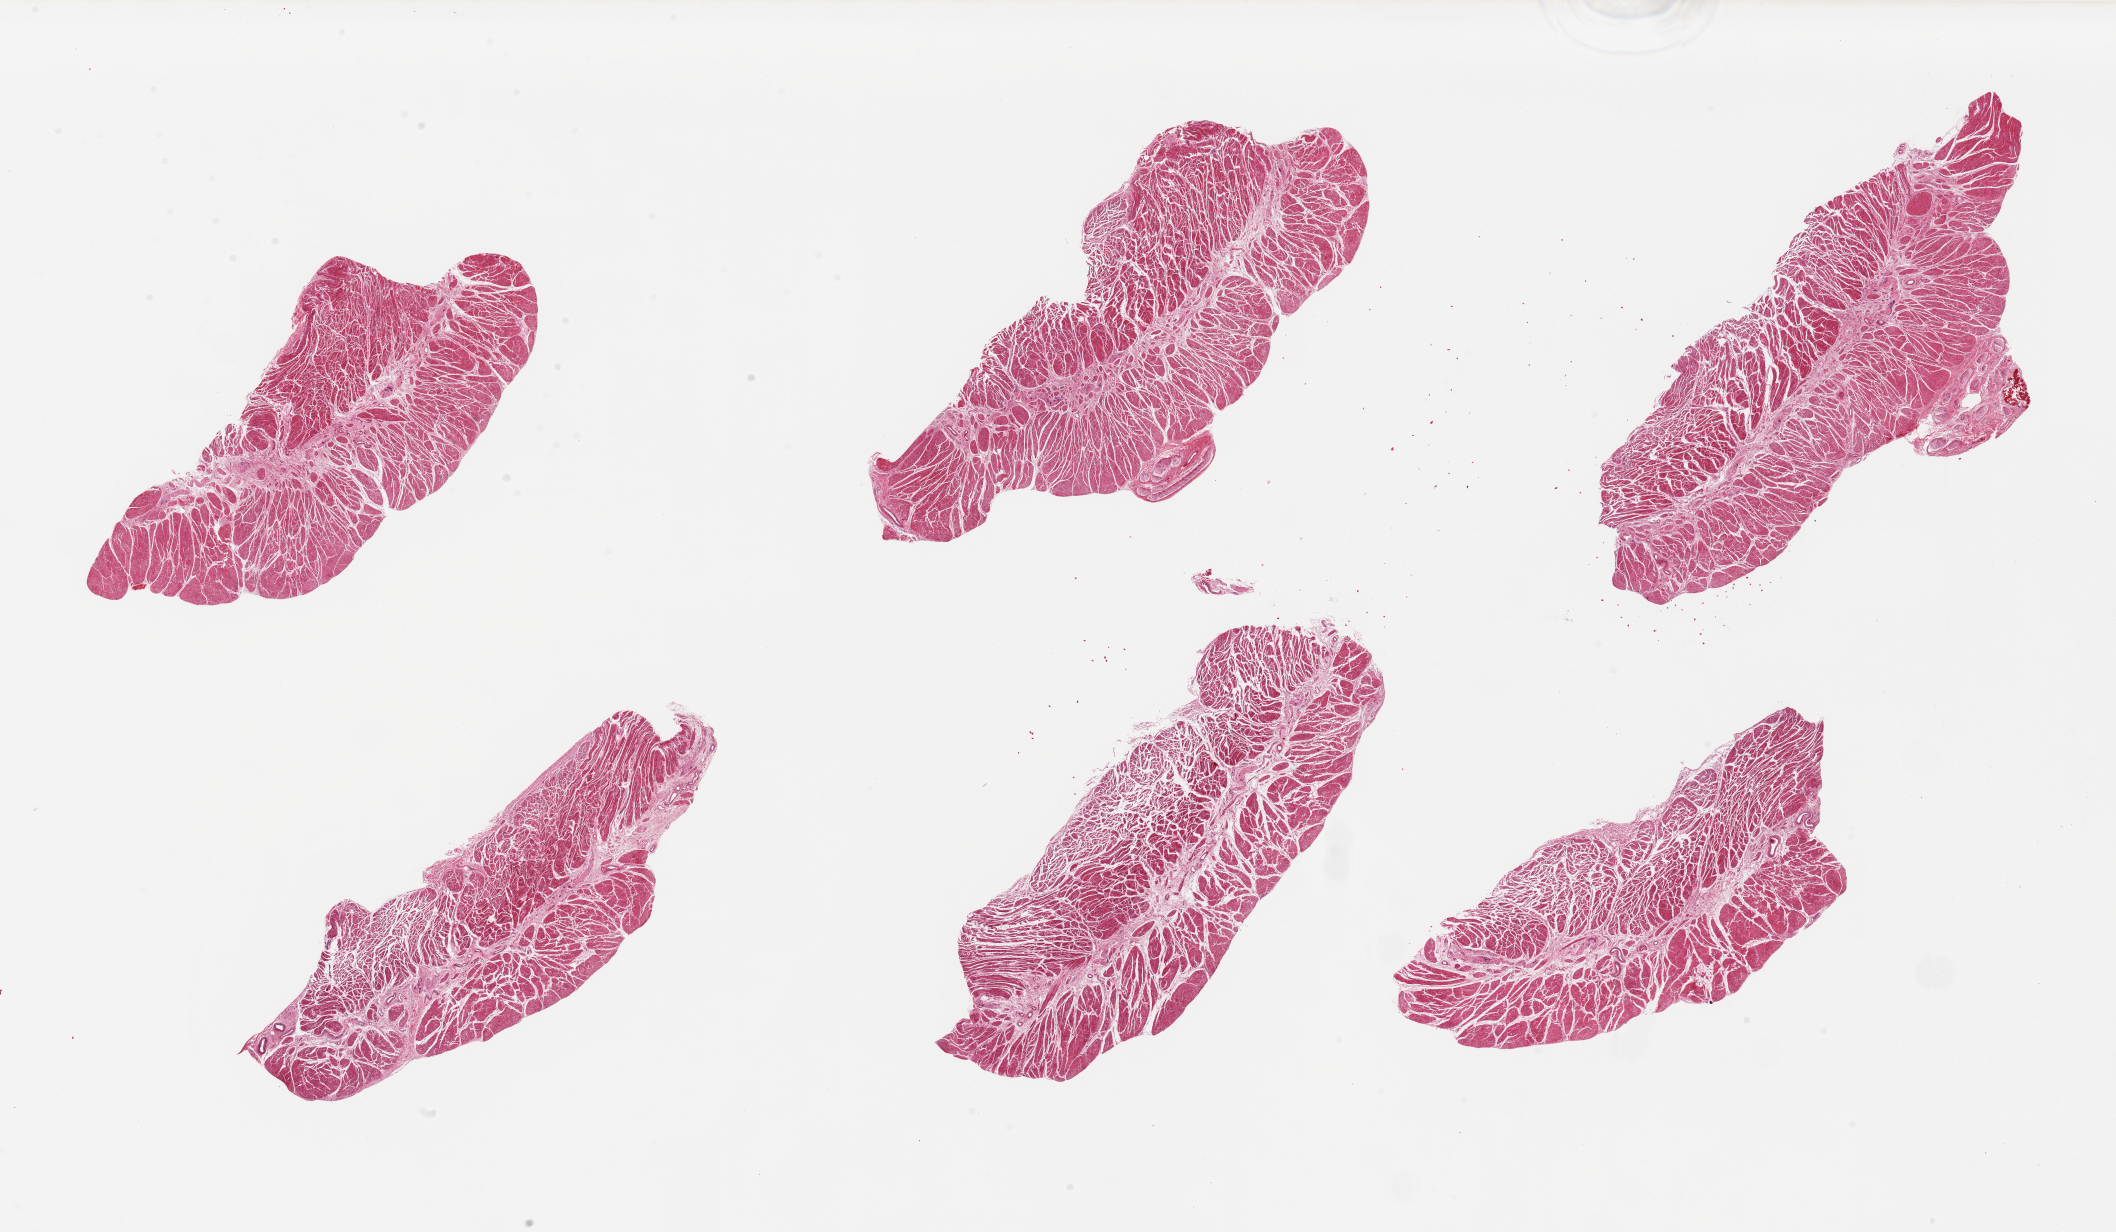
Whole-slide image, hematoxylin and eosin (H&E) stain, shown as a low-resolution overview of the whole scanned area (about 33.5 x 19.5 mm); PAXgene-fixed, paraffin-embedded tissue; section of esophageal muscle (target tissue); tissue donor sample.
* pathologist's review note for this sample: 6 pieces, all muscularis, good speicmens